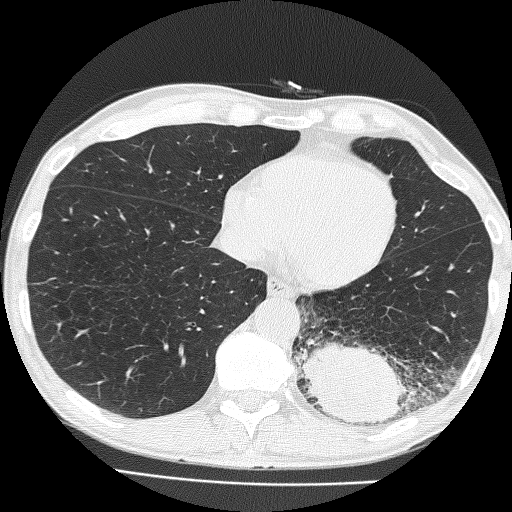
Low-dose screening chest CT, one axial slice; slice 54 of 160 in the series (ordered by position); reconstruction kernel FC51; lung window (W 1500 / L -600 HU); 2 mm slice thickness; 512 × 512 image matrix, field of view 324 × 324 mm.
Annotated regions visible in this slice (manually delineated by an expert):
- lesion 1 (tumor, lower lobe of left lung): bounding box [x1, y1, x2, y2] px = [296, 342, 411, 426]